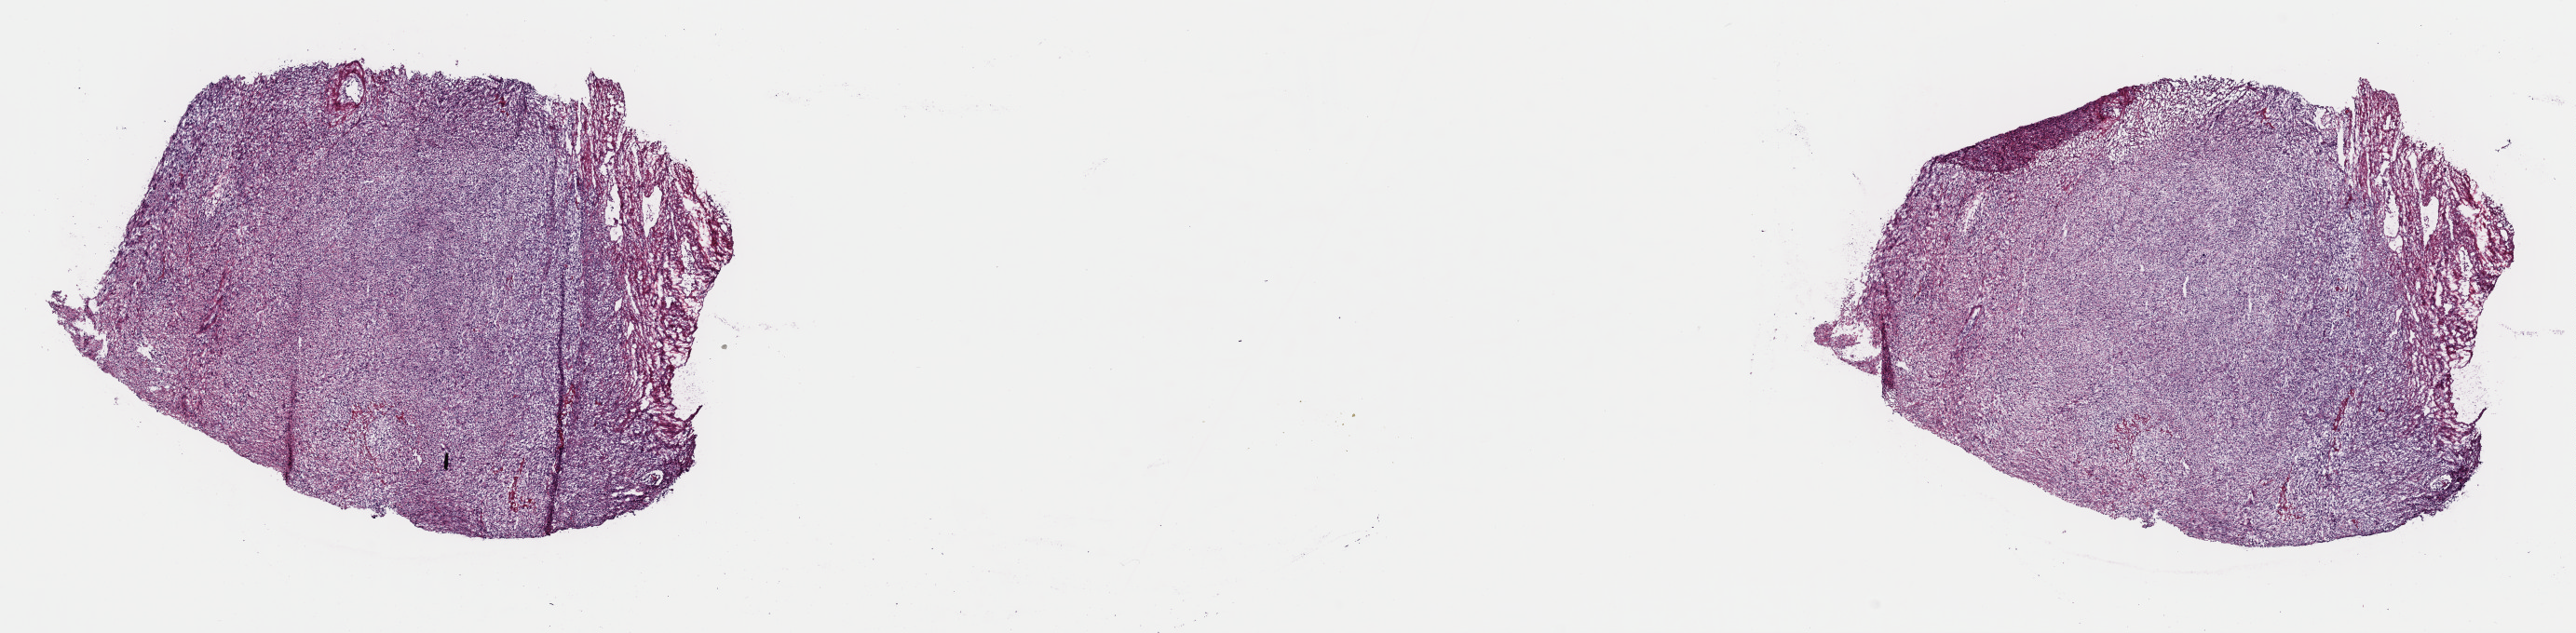
Whole-slide histology image, Hematoxylin and eosin (H&E) stained, shown as a low-resolution overview of the whole scanned area (about 21.9 x 5.4 mm), frozen section, sample: primary tumour, uterus. Patient: female, age at initial diagnosis 71 years. Composition of this section per pathologist review: tumour cells 98%, tumour nuclei 85%, normal cells 0%, stromal cells 0%, necrosis 2%. Infiltration values recorded for this section: lymphocyte infiltration 2%, monocyte infiltration 0%, neutrophil infiltration 0%.
- diagnosis: Leiomyosarcoma, NOS